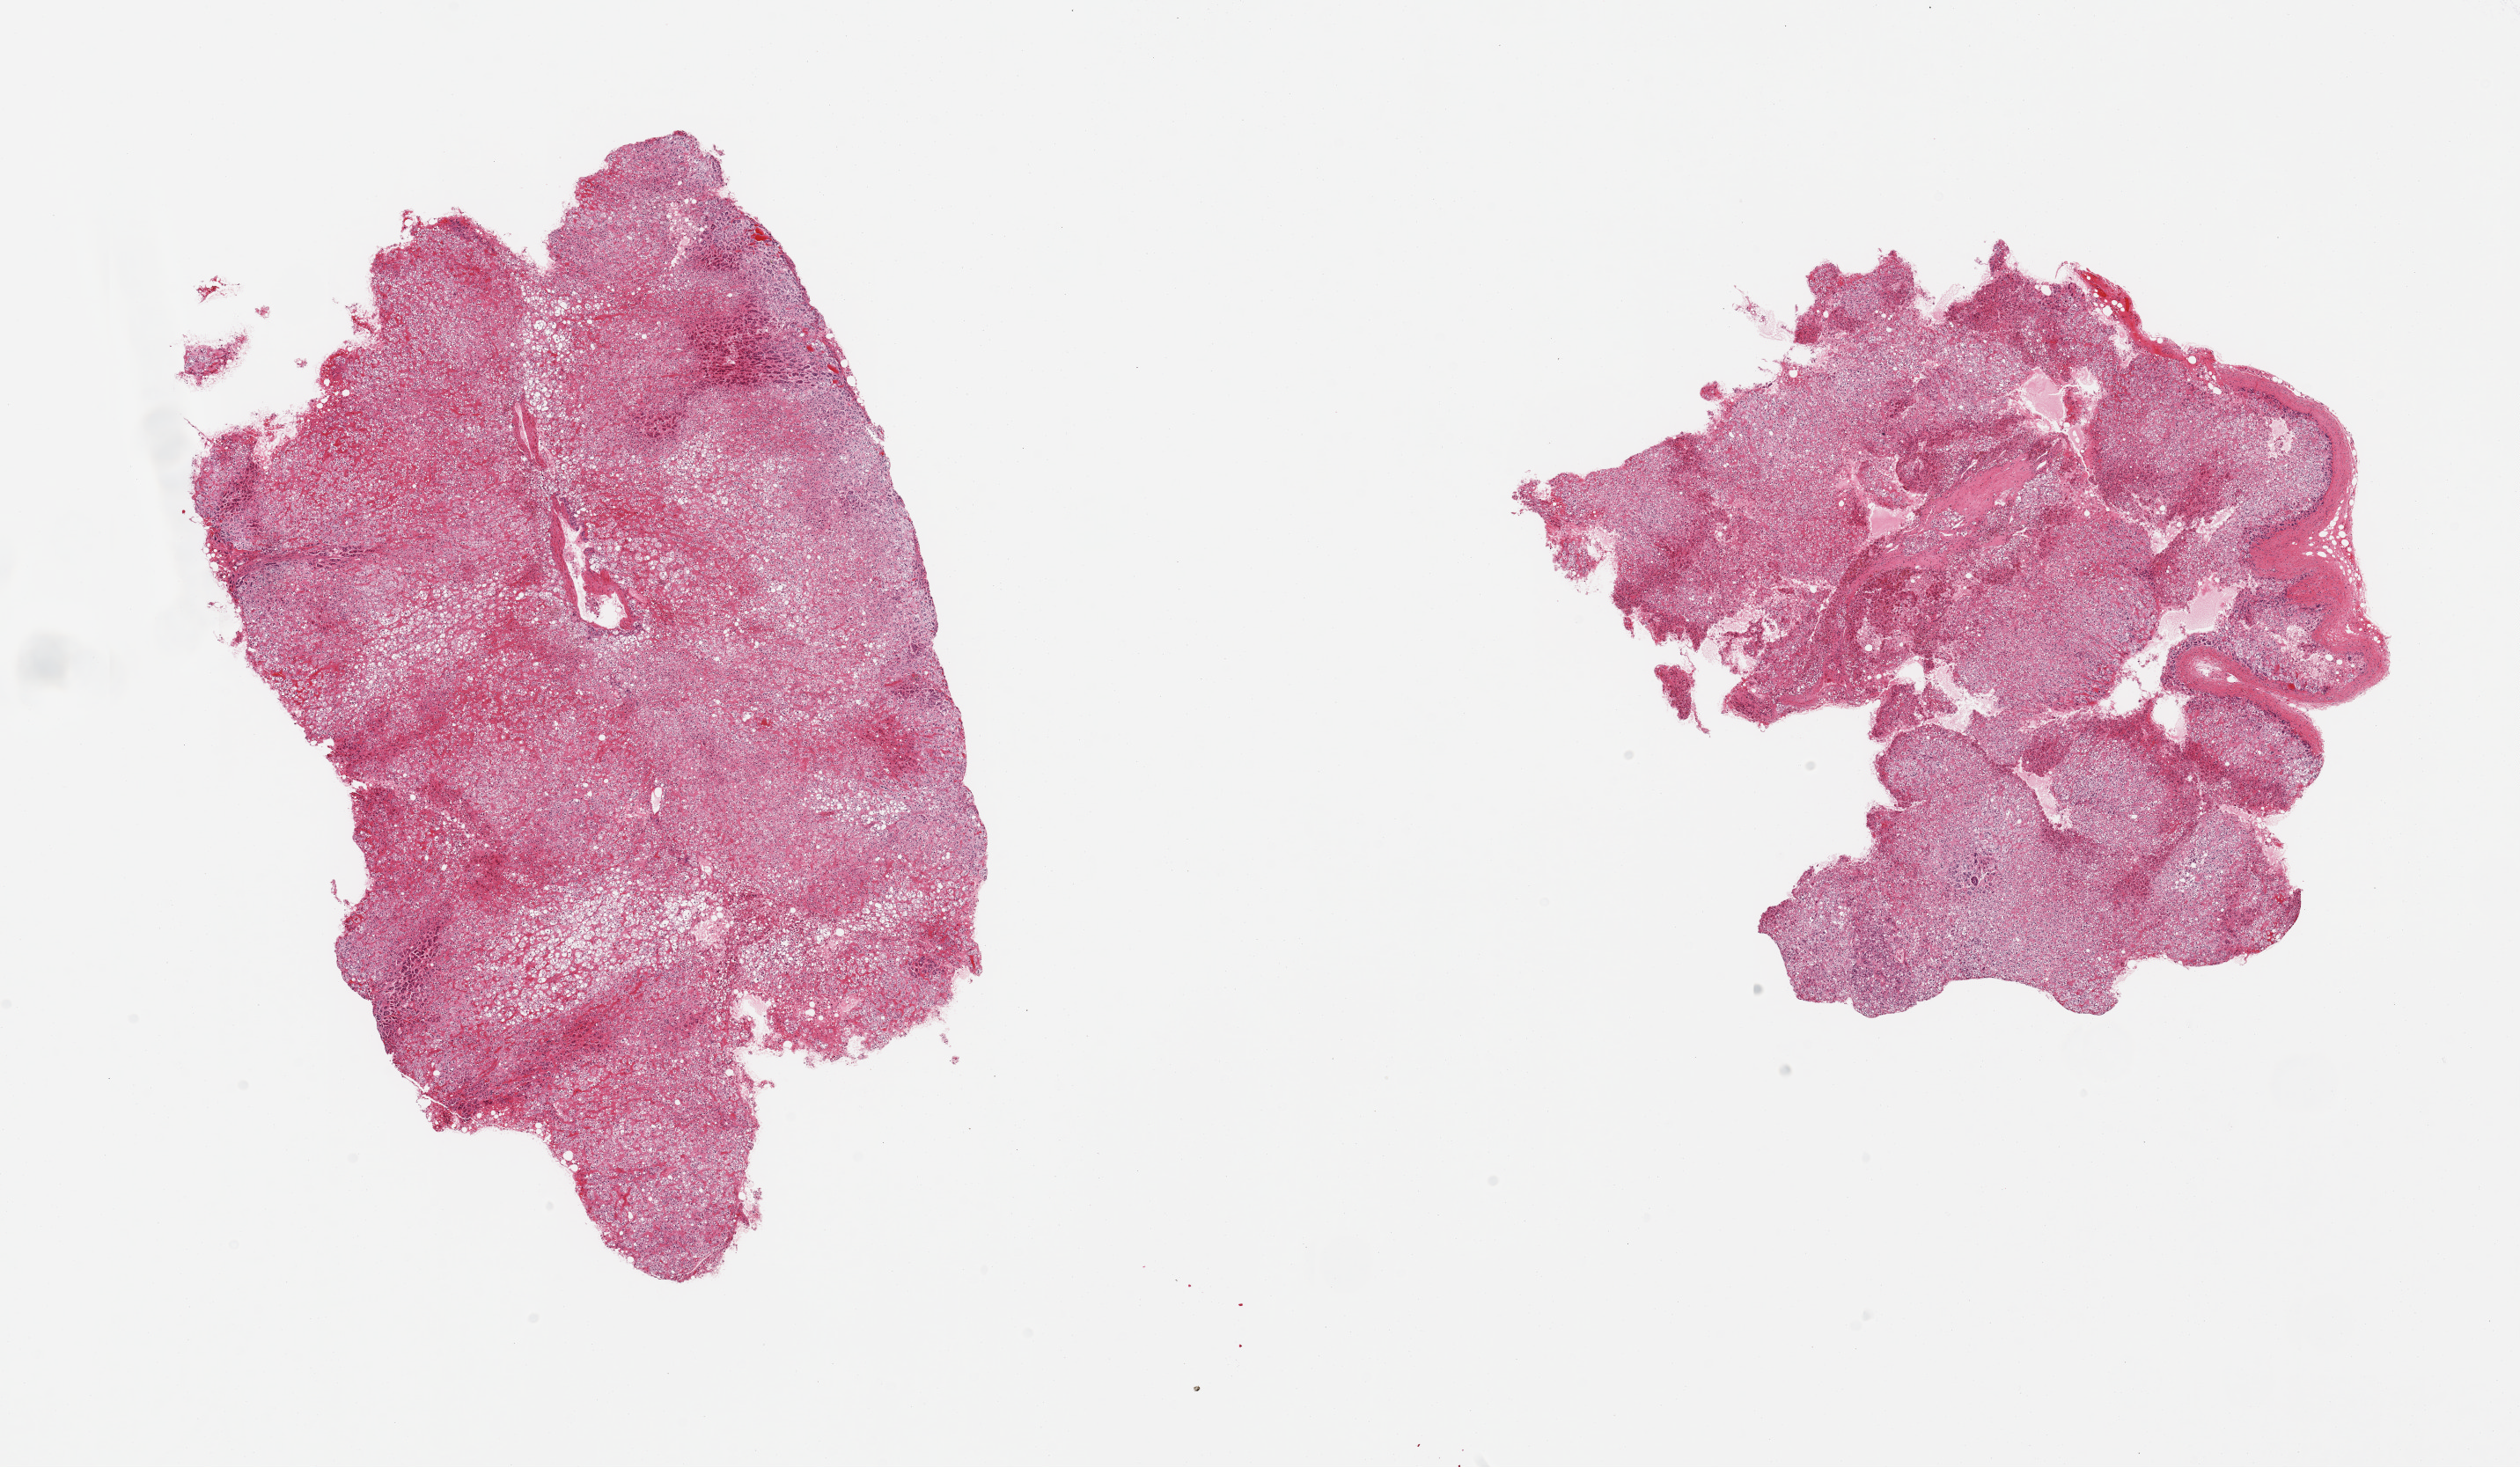
Whole-slide image, hematoxylin and eosin (H&E) stain, whole scanned area (about 22.6 x 13.2 mm, acquisition: 20x scan) shown as a low-resolution overview, PAXgene-fixed paraffin-embedded (PFPE) section, section of adrenal gland (target tissue), tissue donor sample.
* reviewer comment on this tissue sample: 2 pieces, all cortex